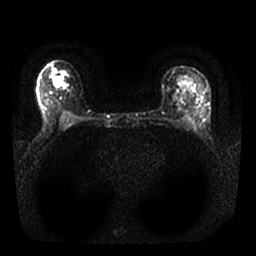
Breast MRI, one axial slice. Diffusion-weighted series; image 2 of 4 stored at this slice position (different b-values; order by instance number). 1.5 T. 4 mm slice thickness. 256 × 256 image matrix, field of view 310 × 310 mm. Female patient.
Annotated regions visible in this slice (manually delineated by an expert):
- tumour on diffusion-weighted imaging: box from (x=54, y=77) to (x=58, y=80) px